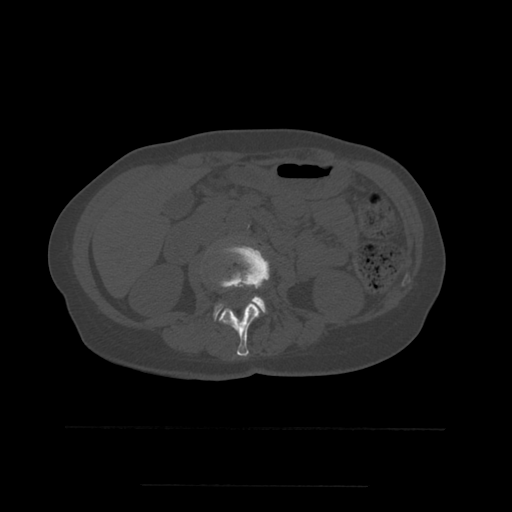
CT including the spine, one axial slice. Position 202 of 544 along the scan axis. Bone window (W 1800 / L 400 HU). 512 × 512 image matrix. Patient age 58 years. From the clinical record (not read from this slice): primary cancer: lung.
Annotated regions visible in this slice (semi-automatic segmentation, software-assisted and operator-edited):
- L2 vertebra: bounding box <215,244,270,357> (left, top, right, bottom; pixels)
- L3 vertebra: <214,296,267,321>